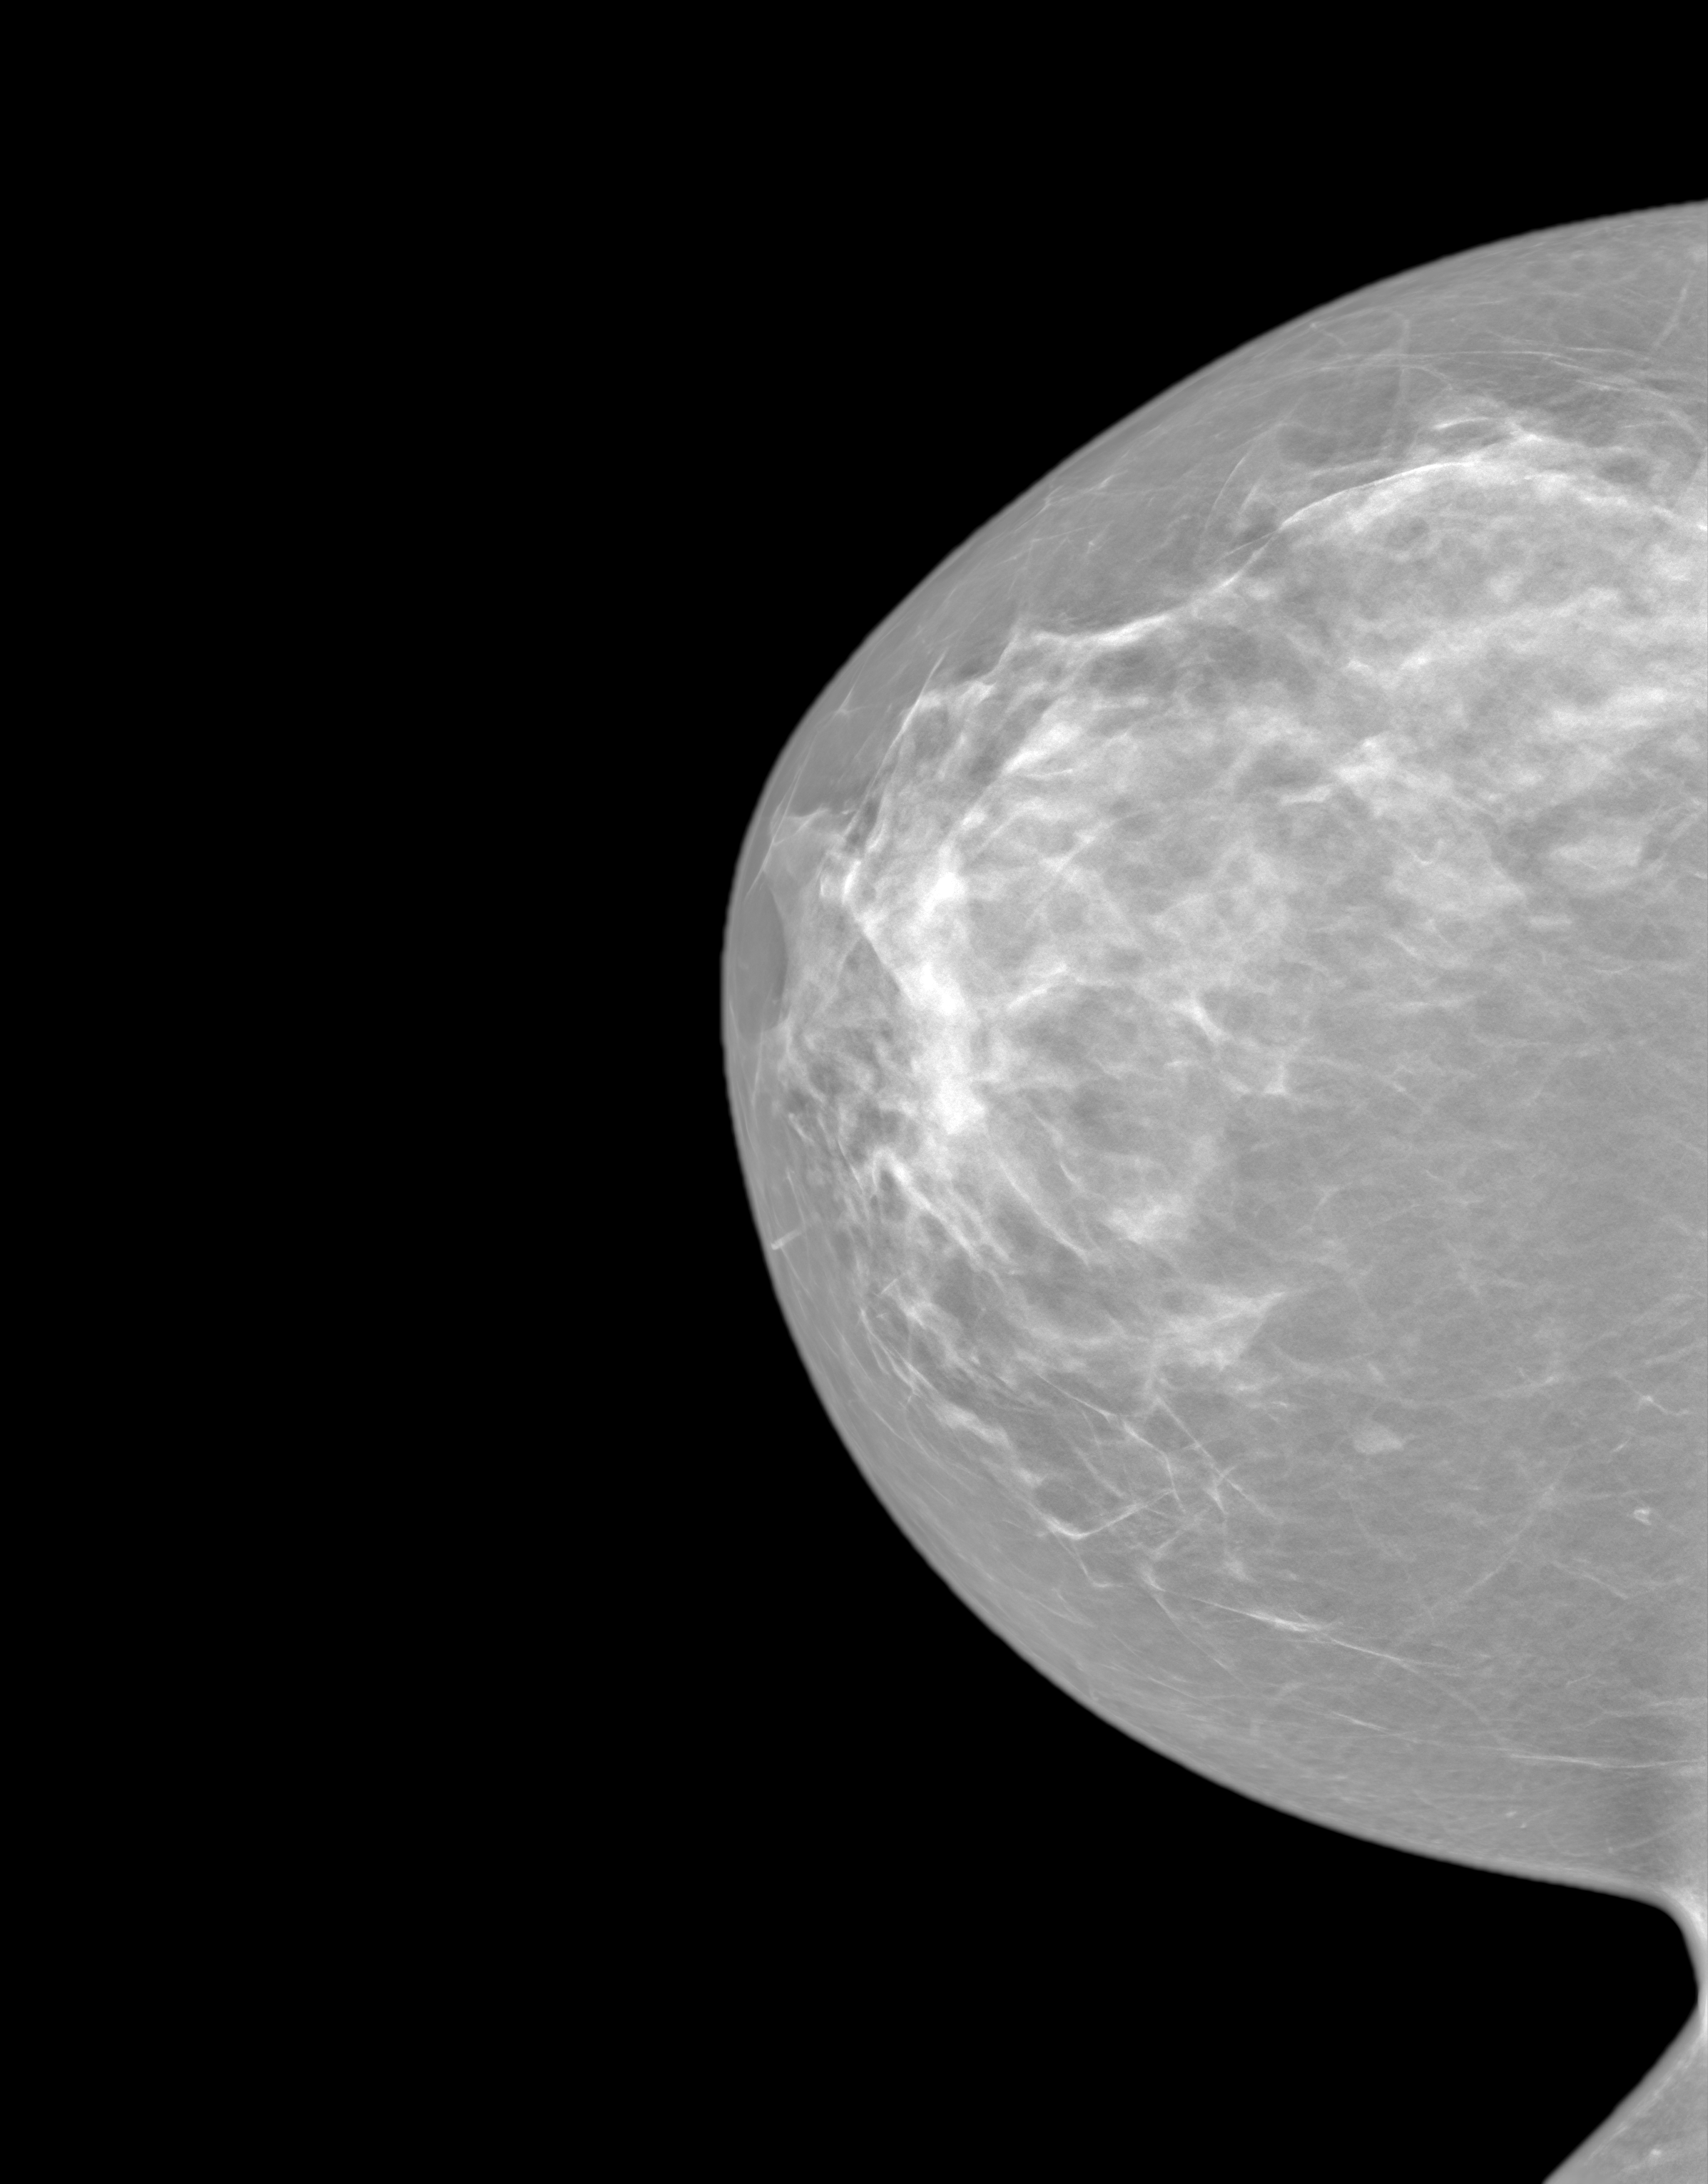
Annual screening mammography examination. Female patient, age 42 years.
Image type: synthesized 2-D view from tomosynthesis. Breast: right. Projection: cranio-caudal projection. Breast density at the screening exam (both breasts): heterogeneously dense (BI-RADS density category c). Final BI-RADS assessment for this screening round (tomosynthesis exam, both breasts): category 1. Recall: no recall after this screen.